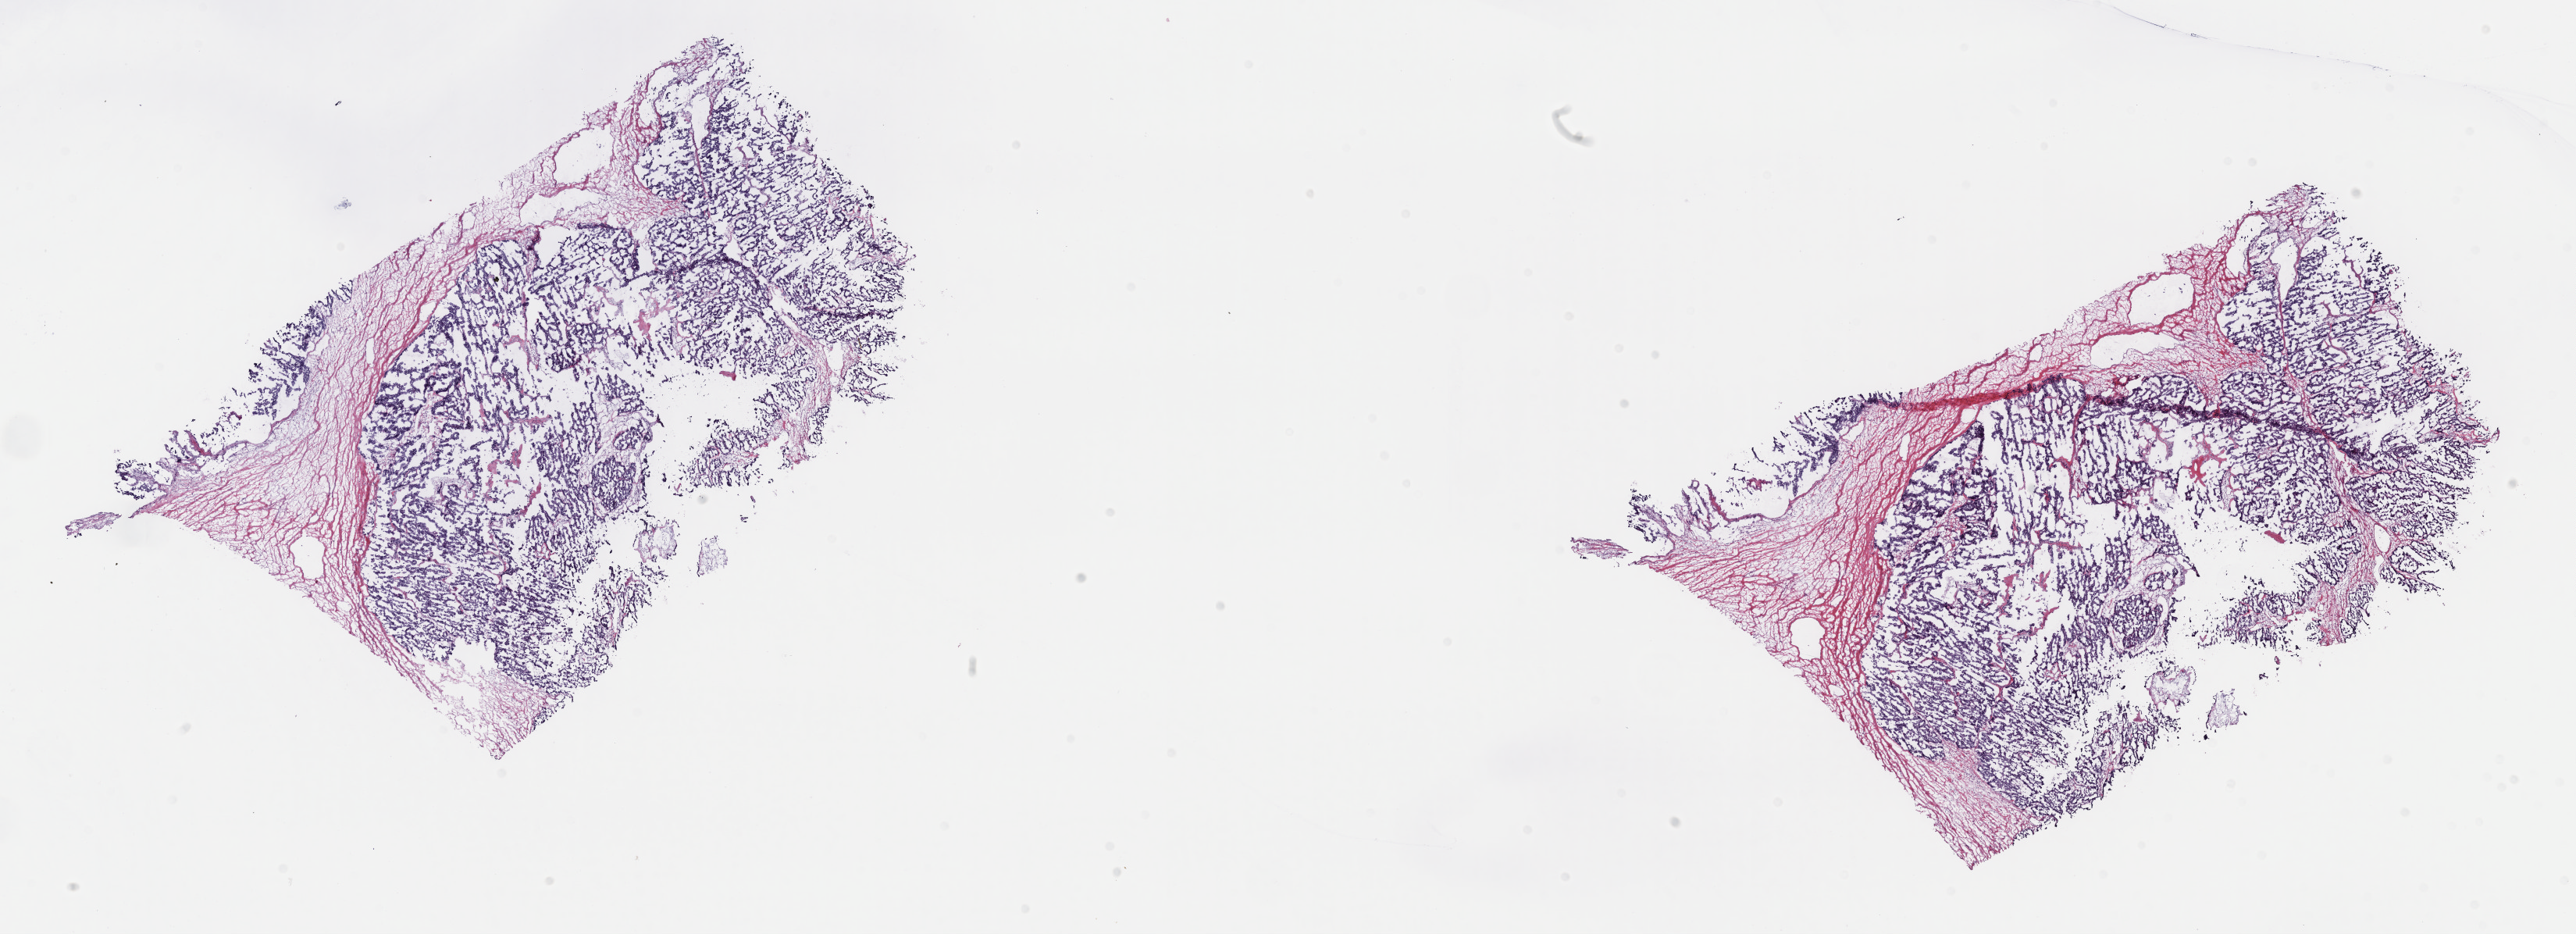
H&E whole-slide image — whole scanned area (about 26.7 x 9.7 mm, slide scanned at 40x) shown as a low-resolution overview; frozen section; sample: primary tumour, ovary. Female patient; age at initial diagnosis 61 years. Histologic grade: GX (grade cannot be assessed). Pathologist review of this section (percent, as recorded): tumour cells 75%, tumour nuclei 75%, normal cells 5%, stromal cells 20%, necrosis 0%. Infiltration values recorded for this section: lymphocyte infiltration 2%, monocyte infiltration 0%, neutrophil infiltration 0%.
* laterality: right
* diagnosis: Papillary serous cystadenocarcinoma
* FIGO stage: IIC